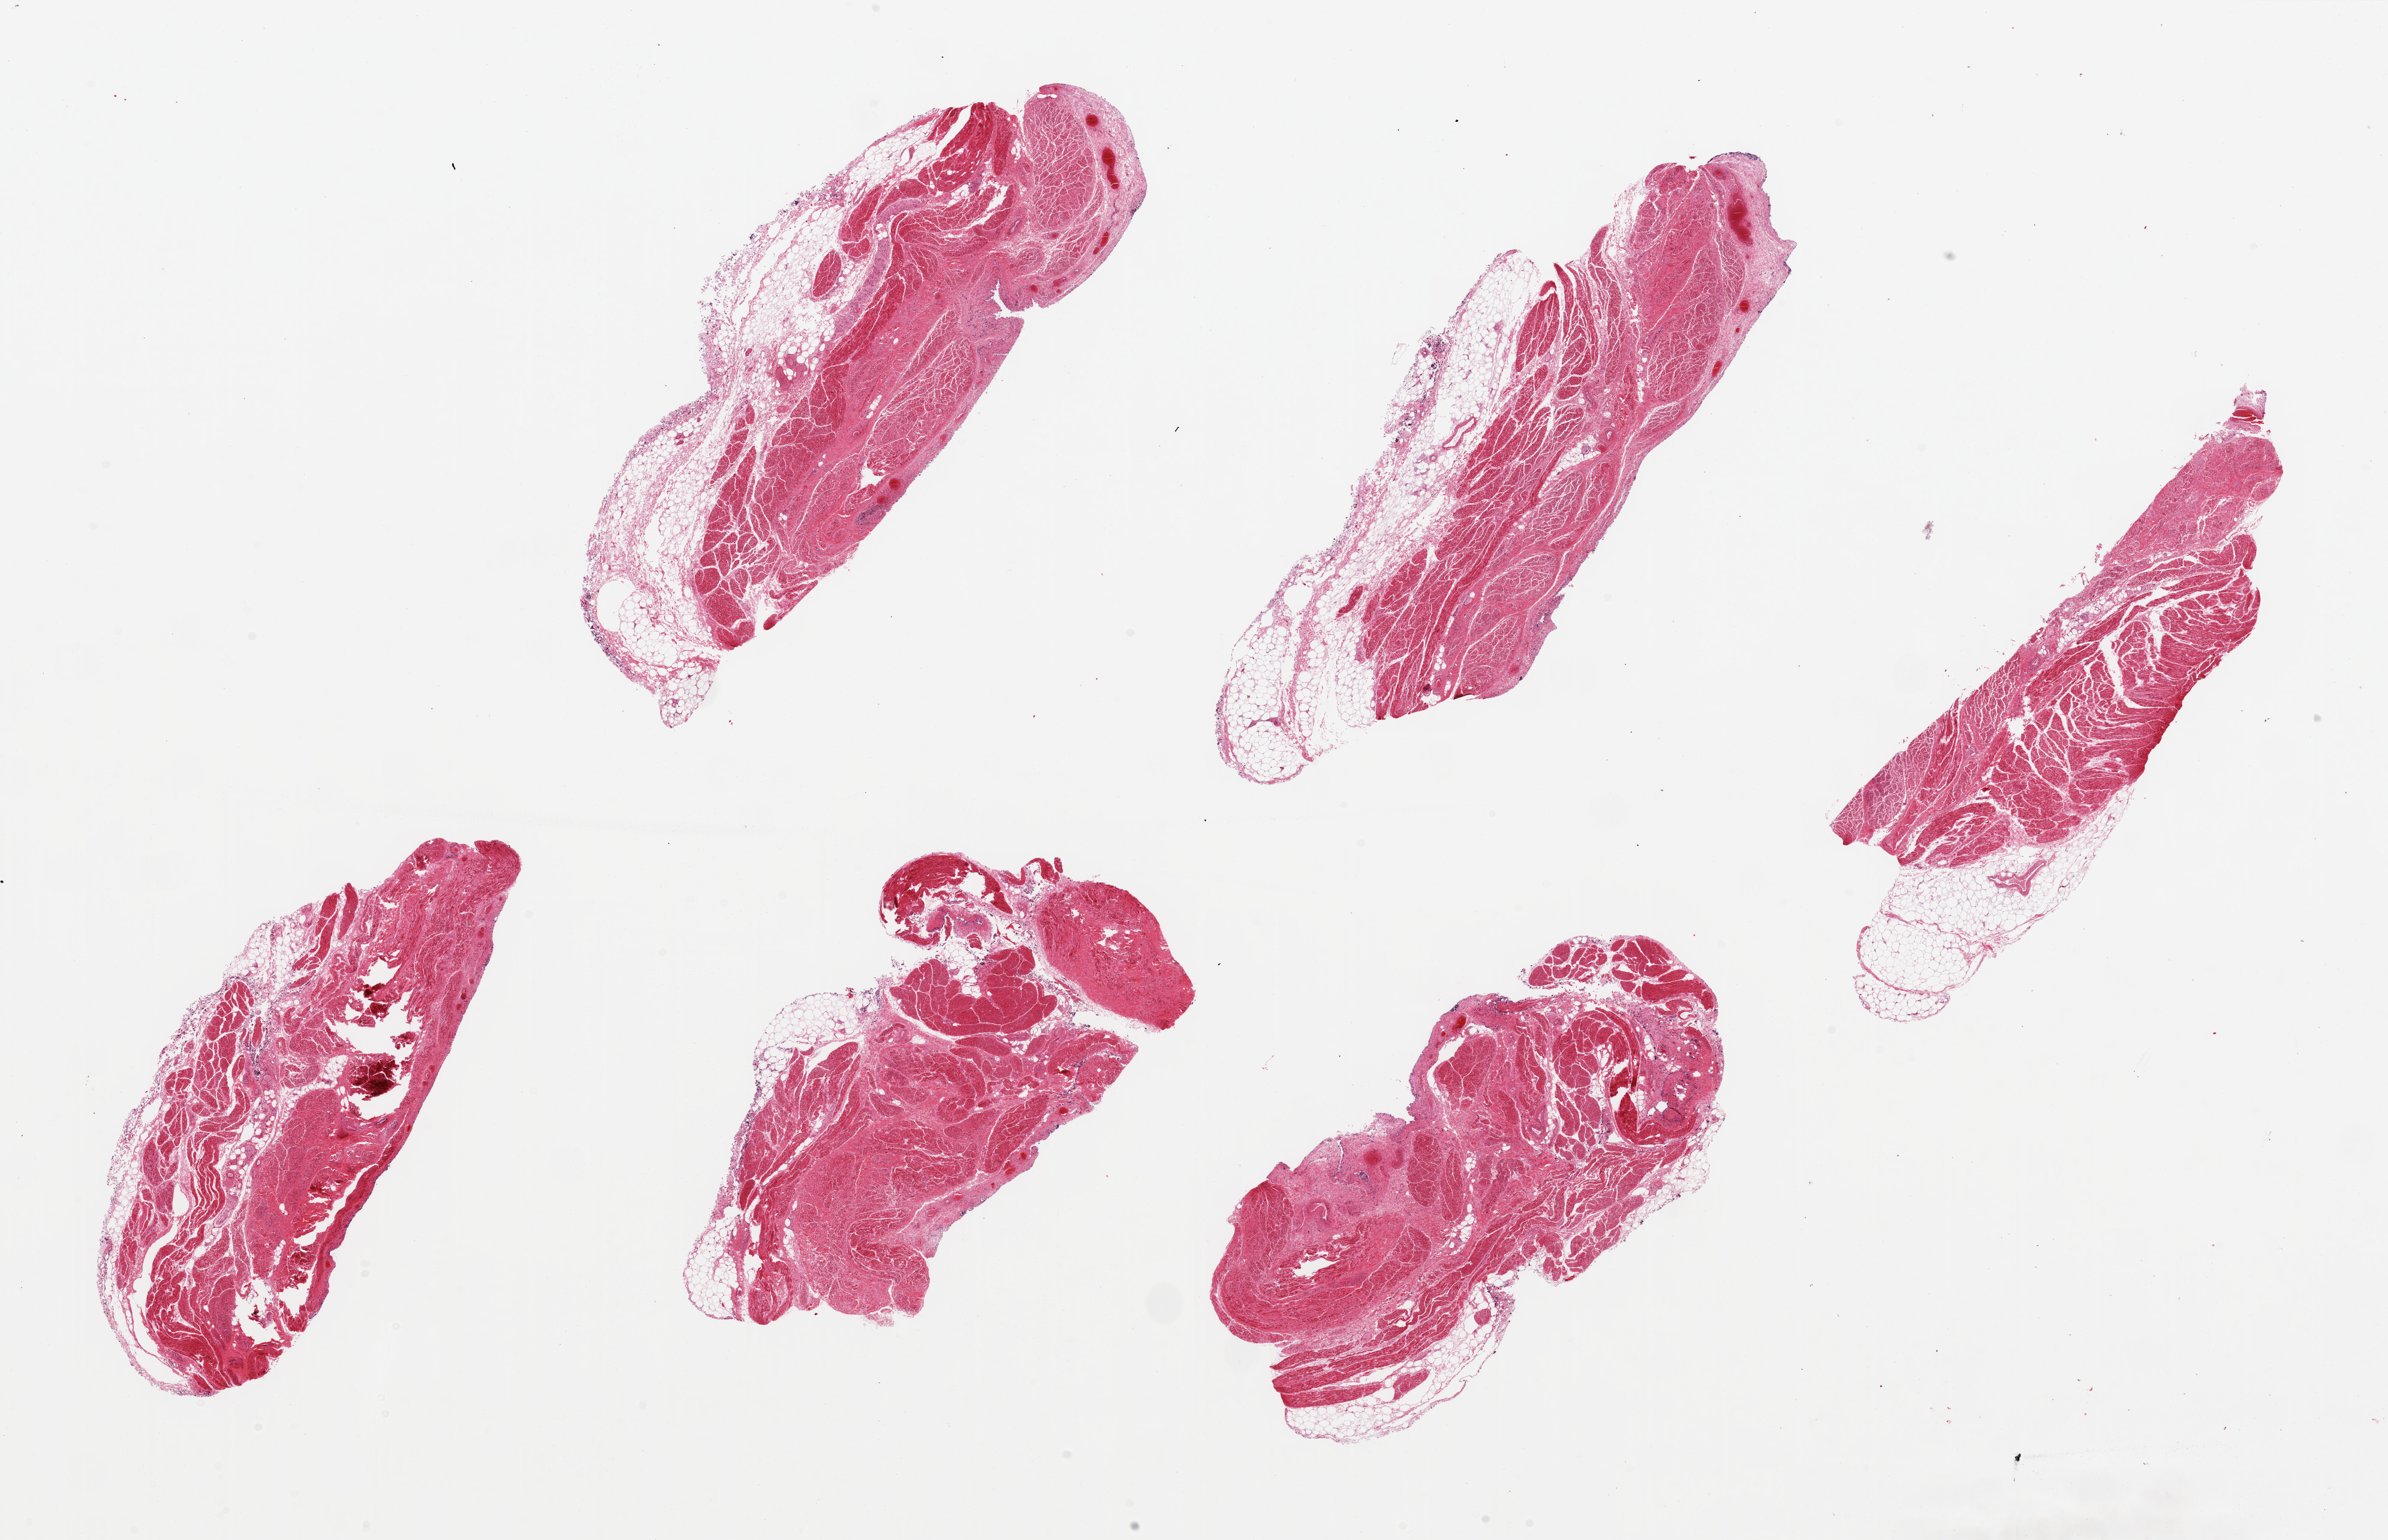
Digitized hematoxylin and eosin (H&E)-stained section, shown as a low-resolution overview of the whole scanned area (about 31.5 x 20.3 mm, slide scanned at 20x). PAXgene-fixed, paraffin-embedded tissue. Sampled site (target tissue): urinary bladder. Donor tissue sample. Male donor.
- reviewer comment on this tissue sample: 6 pieces, ~8x3mm. Urothelium completely sloughed, badly autolyzed